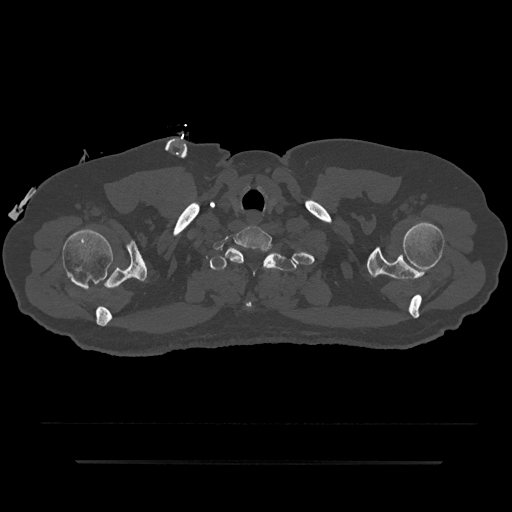
CT including the spine, one axial slice; position 754 of 797 along the scan axis; 120 kVp; bone window (W 1800 / L 400 HU); 0.5 mm slice thickness; 512 × 512 image matrix, field of view 464 × 464 mm. Male patient, age 59 years. From the clinical record (not read from this slice): primary cancer: bile ducts; vertebrae with lytic lesions (as recorded): T10.
Outlined on this slice (semi-automatic segmentation, software-assisted and operator-edited):
- T1 vertebra: bounding box (x1, y1, x2, y2) in pixels: (210, 248, 297, 308)